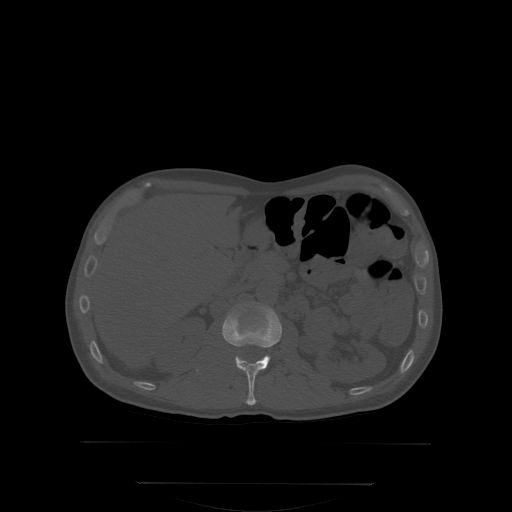
CT including the spine, one axial slice; slice 150 of 350 in the series (ordered by position); bone window (W 1800 / L 400 HU); 512 × 512 image matrix, field of view 500 × 500 mm. Male patient, age 58 years. From the clinical record (not read from this slice): primary cancer: prostate; vertebrae with lytic lesions (as recorded): L1.
Structures marked on this image (semi-automatically segmented with operator editing):
- L1 vertebra: bounding box <224,305,281,405> (left, top, right, bottom; pixels)